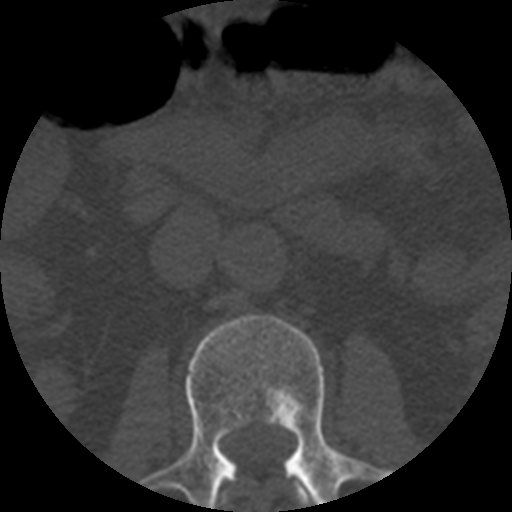
CT including the spine, one axial slice. Slice 156 of 508 in the series (ordered by position). Reconstruction kernel STANDARD. Bone window (W 1800 / L 400 HU). 512 × 512 image matrix, field of view 160 × 160 mm. Patient age 57 years. From the clinical record (not read from this slice): primary cancer: prostate.
Annotated regions visible in this slice (semi-automatically segmented with operator editing):
- L1 vertebra: bounding box (x1, y1, x2, y2) in pixels: (222, 484, 313, 505)
- L2 vertebra: (139, 314, 391, 512)